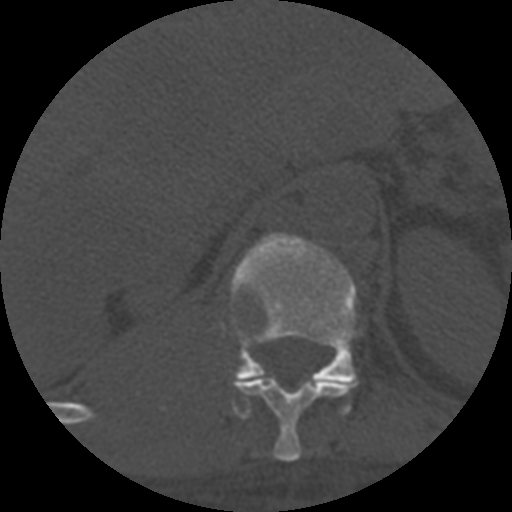
CT including the spine, one axial slice; slice 324 of 708 in the series (ordered by position); 120 kVp; one of 3 acquisitions stored at this slice position; bone window (W 1800 / L 400 HU); 1.25 mm slice thickness; 512 × 512 image matrix. Patient age 55 years. From the clinical record (not read from this slice): primary cancer: colon; vertebrae with lytic lesions (as recorded): T12, L1, L5.
Outlined on this slice (semi-automatic segmentation, software-assisted and operator-edited):
- T11 vertebra: bounding box (x1, y1, x2, y2) in pixels: (232, 379, 352, 462)
- T12 vertebra: (230, 233, 359, 414)